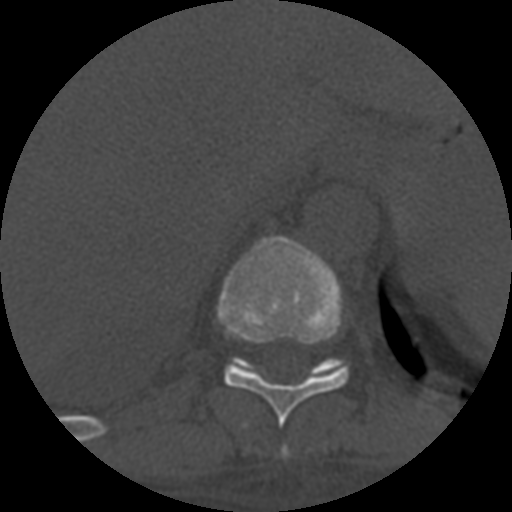
CT including the spine, one axial slice. Slice 352 of 708 in the series (ordered by position). Reconstruction kernel STANDARD. One of 3 acquisitions stored at this slice position. Bone window (W 1800 / L 400 HU). 1.25 mm slice thickness. 512 × 512 image matrix. Patient age 55 years. Case-level facts recorded for this patient, not image findings: primary cancer: colon; vertebrae with lytic lesions (as recorded): T12, L1, L5.
Annotated regions visible in this slice (semi-automatic segmentation, software-assisted and operator-edited):
- T10 vertebra: box from (x=217, y=238) to (x=350, y=427) px
- T11 vertebra: (x=228, y=358)–(x=348, y=378)
- T9 vertebra: (x=282, y=448)–(x=288, y=457)